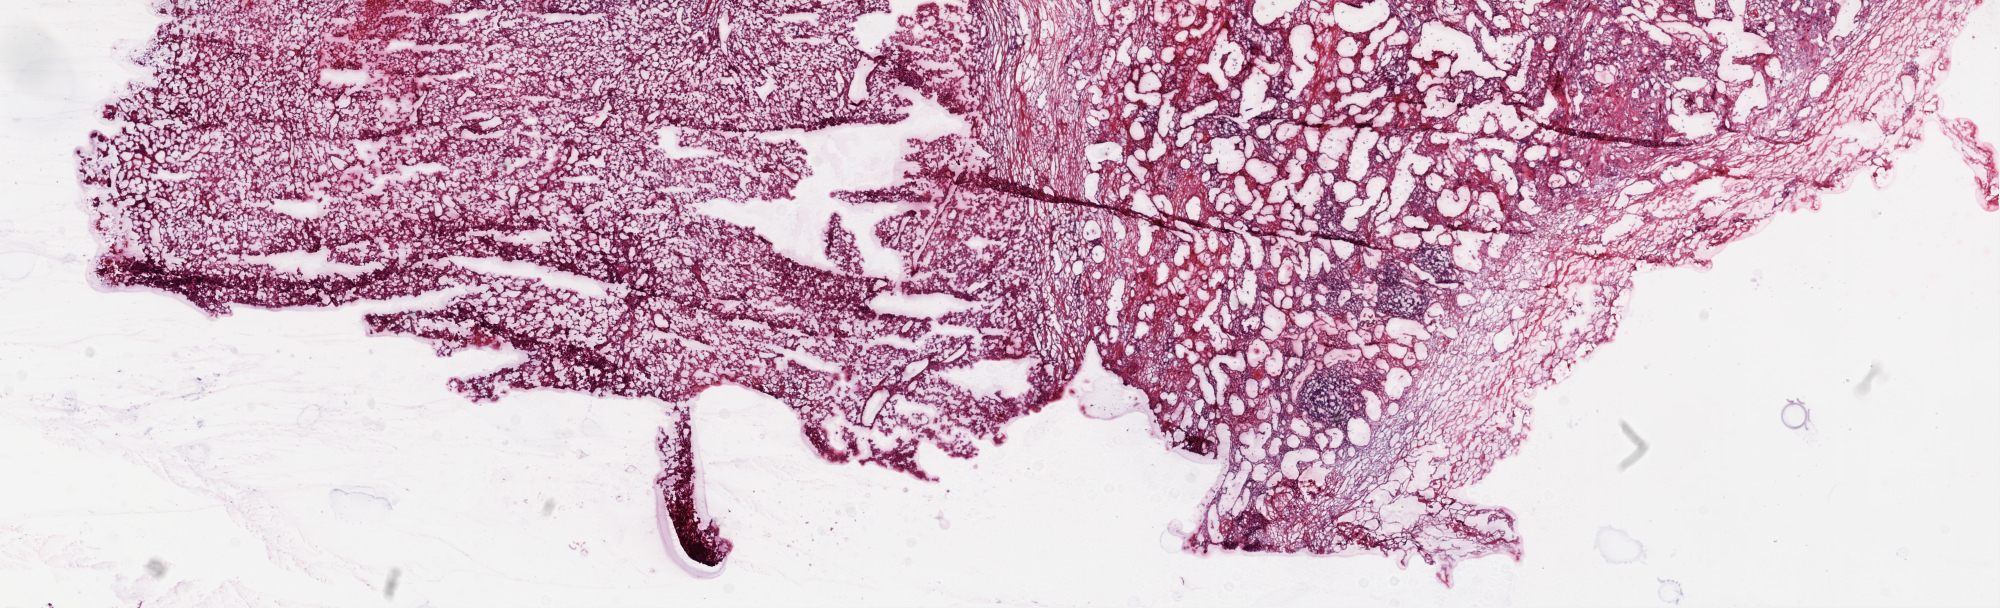
Whole-slide histology image, H&E, shown as a low-resolution overview of the whole scanned area (about 16.0 x 4.9 mm); frozen section from the top of the tissue portion; kidney, primary tumour sample. Female patient; age at initial diagnosis 60 years. Histologic grade: G4 (undifferentiated). Slide review estimates, as recorded: tumour cells 90%, tumour nuclei 85%, normal cells 0%, stromal cells 10%, necrosis 0%.
AJCC pathologic stage: IV. Pathologic diagnosis: Clear cell adenocarcinoma, NOS. TNM: T3b NX M1.